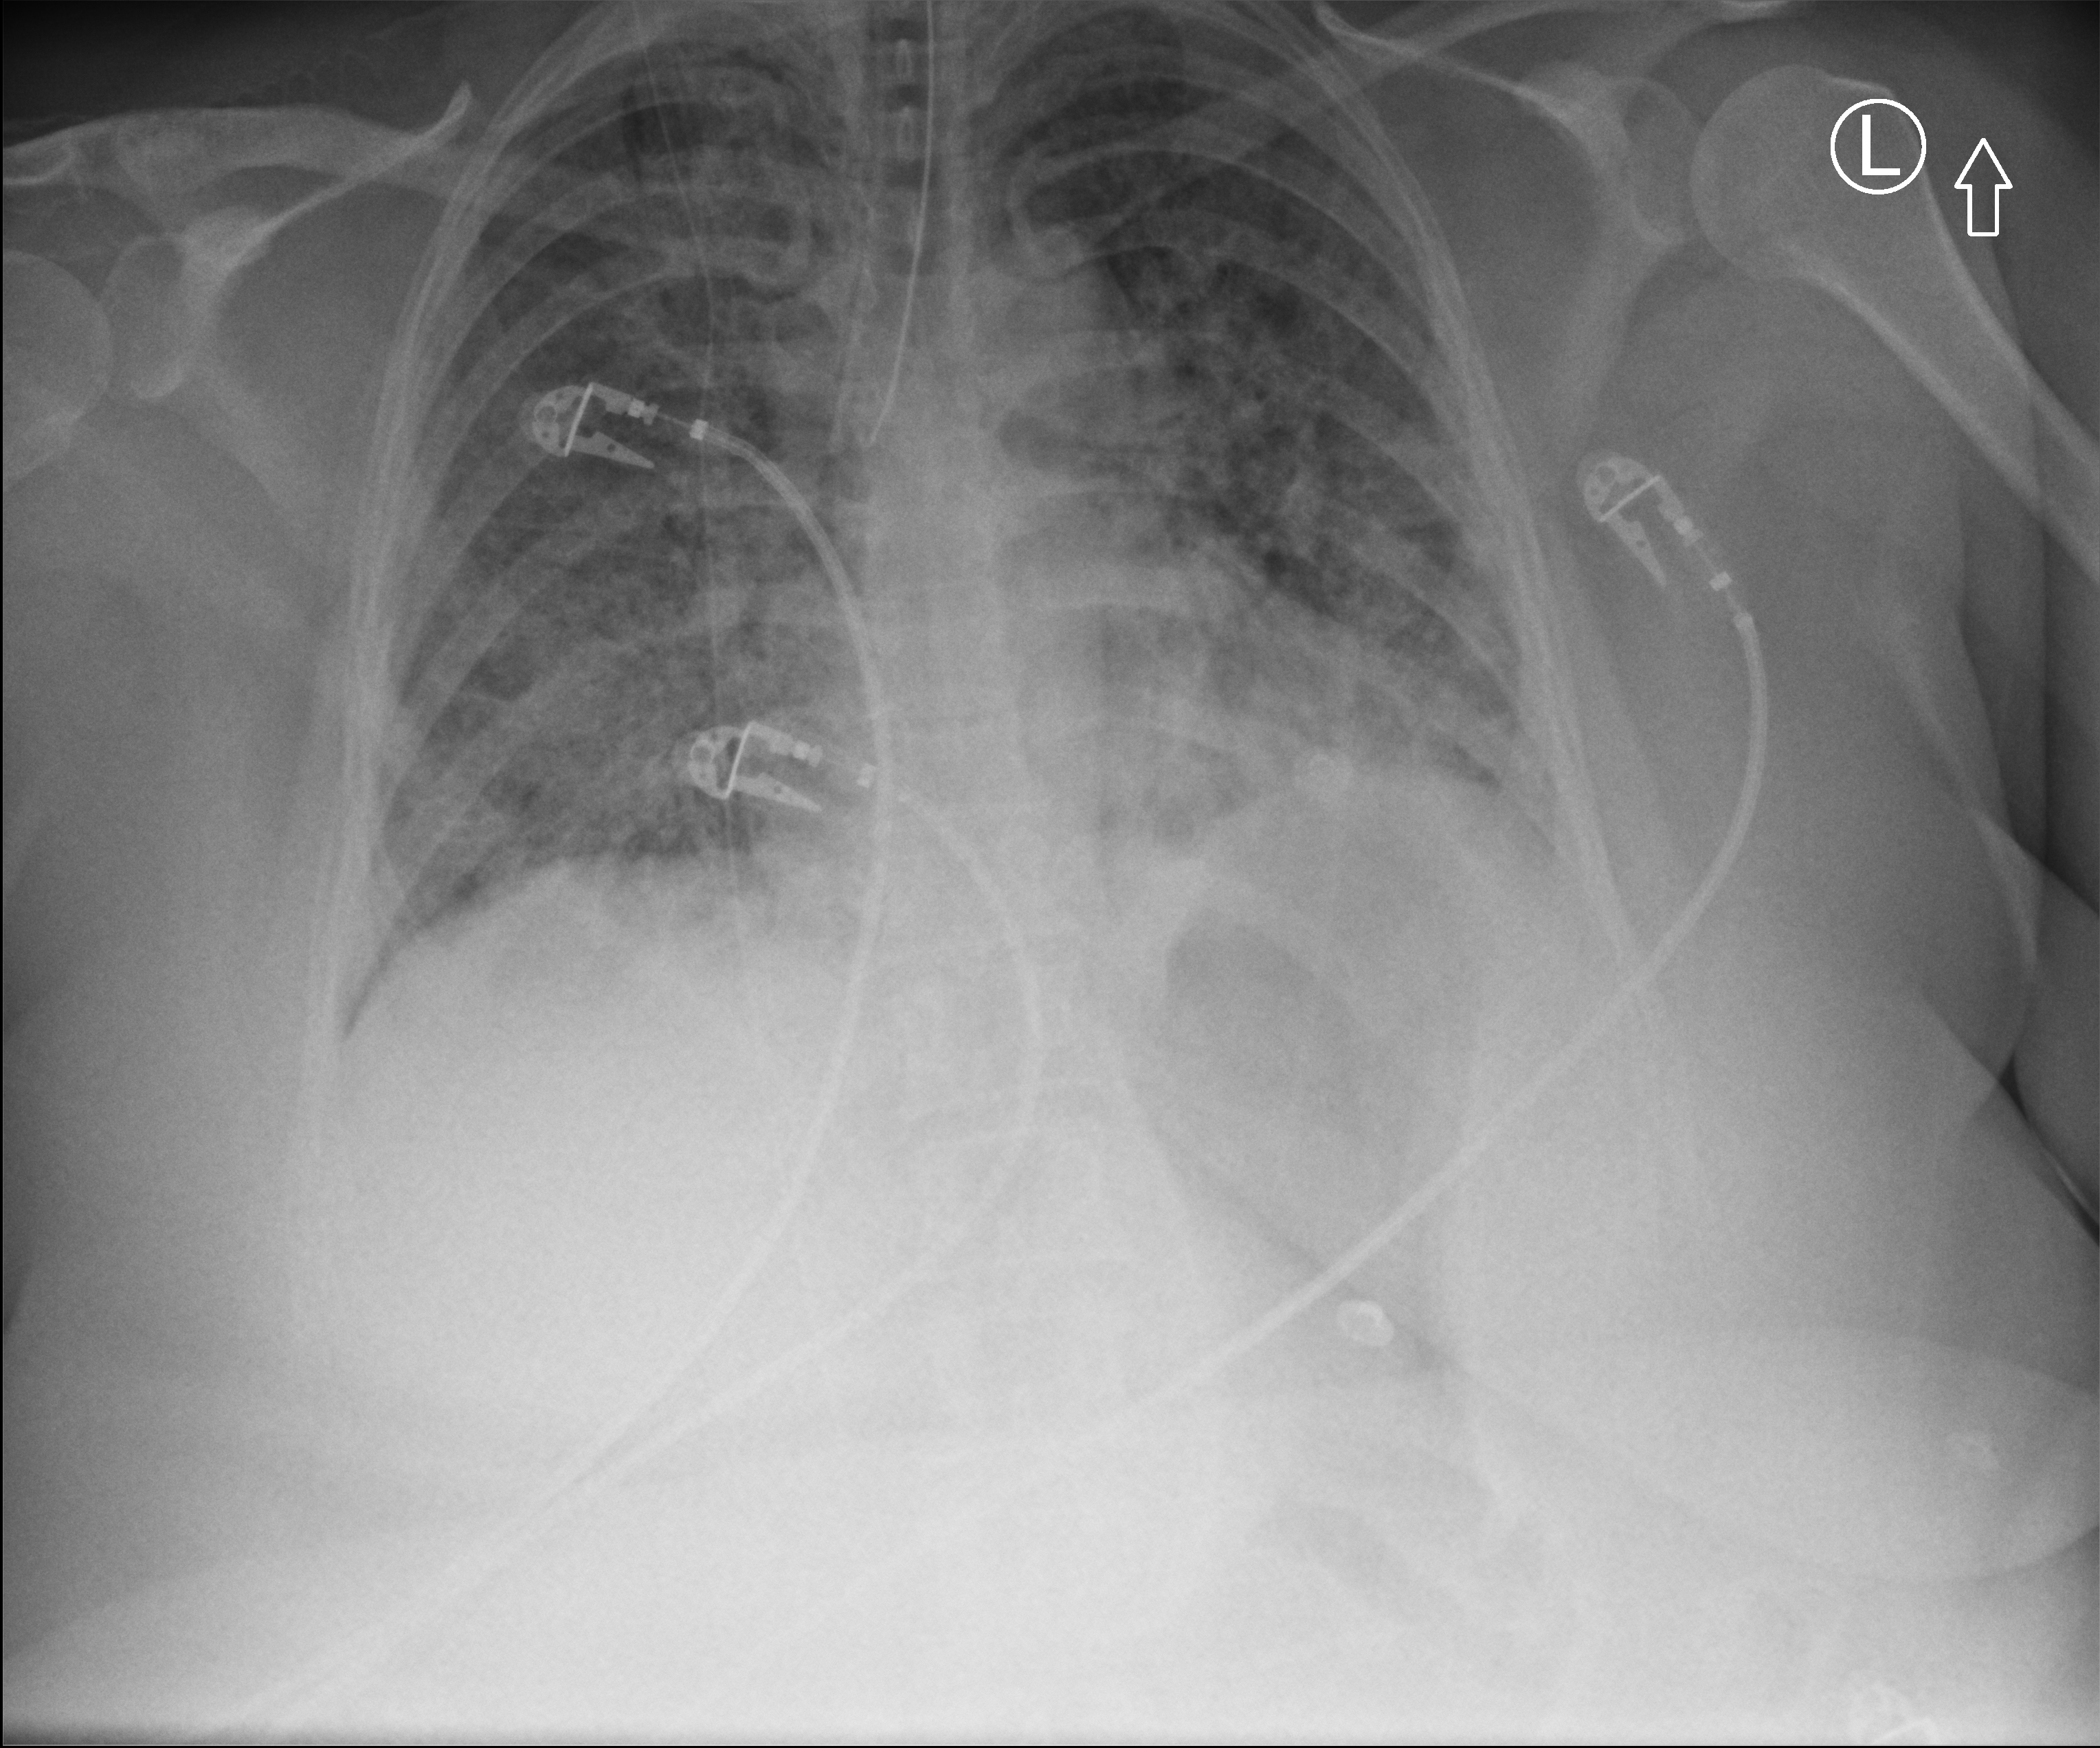
Bedside chest radiograph (computed radiography); anteroposterior (AP) projection. Patient hospitalised with COVID-19; female, aged 18–59 years.
Hospital-stay facts (about this admission, not read from this image; timing relative to this image not recorded): other chronic lung disease (admission record): no; admitted to intensive care during this hospital stay: yes; mechanically ventilated during this hospital stay: yes.